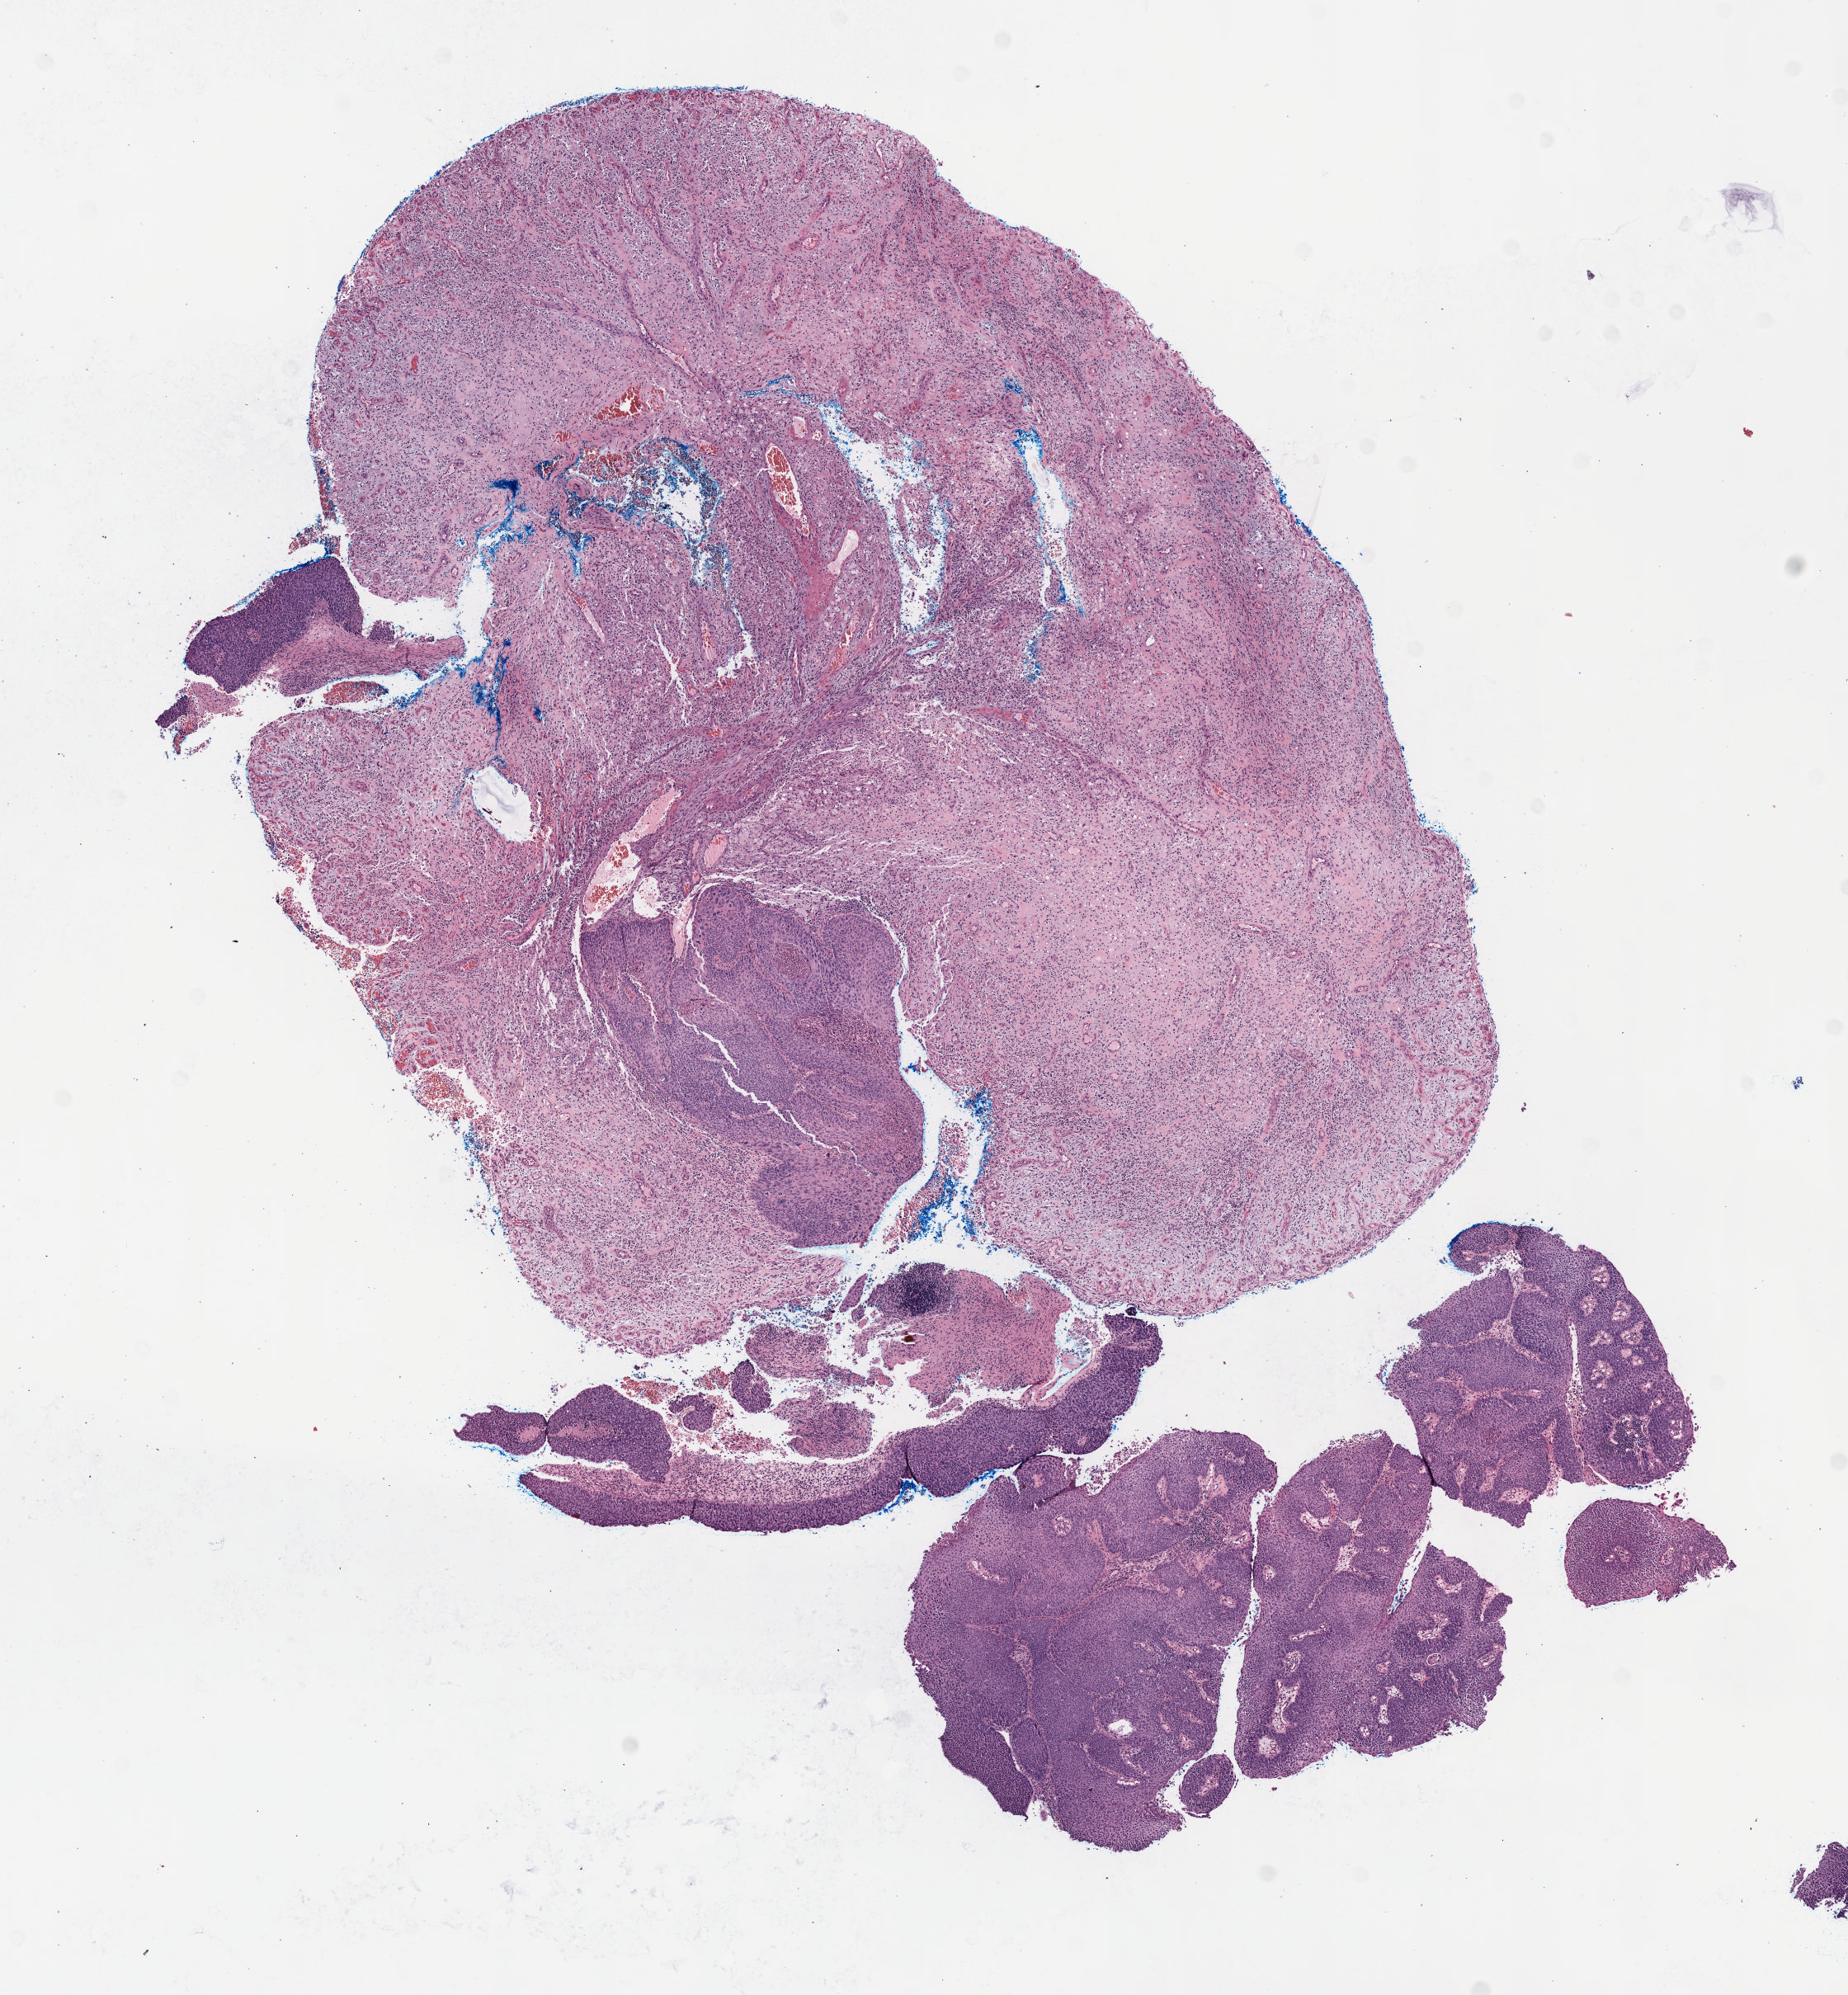
H&E whole-slide image, shown as a low-resolution overview of the whole scanned area (about 9.1 x 9.8 mm, from a 40x scan); formalin-fixed paraffin-embedded (FFPE) diagnostic section; sample: primary tumour, cervix. Female patient; age at initial diagnosis 74 years. Histologic grade: GX (grade cannot be assessed).
Diagnosis: Squamous cell carcinoma, NOS (cervix uteri). FIGO stage: IVA.